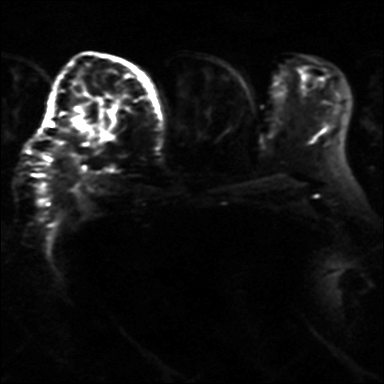
Breast MRI, one axial slice. Slice 20 of 36 in the series (ordered by position). Diffusion-weighted series; image 2 of 4 stored at this slice position (different b-values; order by instance number). 3 T. 4 mm slice thickness. 384 × 384 image matrix. Female patient.
Structures marked on this image (outlined manually by an expert reader):
- tumour on diffusion-weighted imaging: bounding box [x1, y1, x2, y2] px = [70, 116, 86, 131]